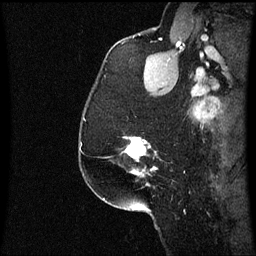
Breast MRI (dynamic contrast-enhanced), one sagittal slice; position 47 of 60 along the scan axis; dynamic contrast-enhanced series, image 2 of 3 at this slice position (ordered by acquisition); 1.5 T; TE 4.2 ms, TR 8.9 ms; 2 mm slice thickness; 256 × 256 image matrix, field of view 200 × 200 mm. Female patient, age 58 years. From the clinical record (not read from this slice): setting: breast cancer imaged before/during neoadjuvant chemotherapy; receptor status: triple-negative.
Annotated regions visible in this slice (semi-automatically segmented with operator editing):
- analysis volume of interest (the breast-tissue region the enhancement analysis was run in; not a lesion): box from (x=114, y=138) to (x=157, y=177) px
- tumour enhancement mask (voxels above the 70 % enhancement threshold inside the analysis volume of interest): (x=126, y=138)–(x=155, y=175)